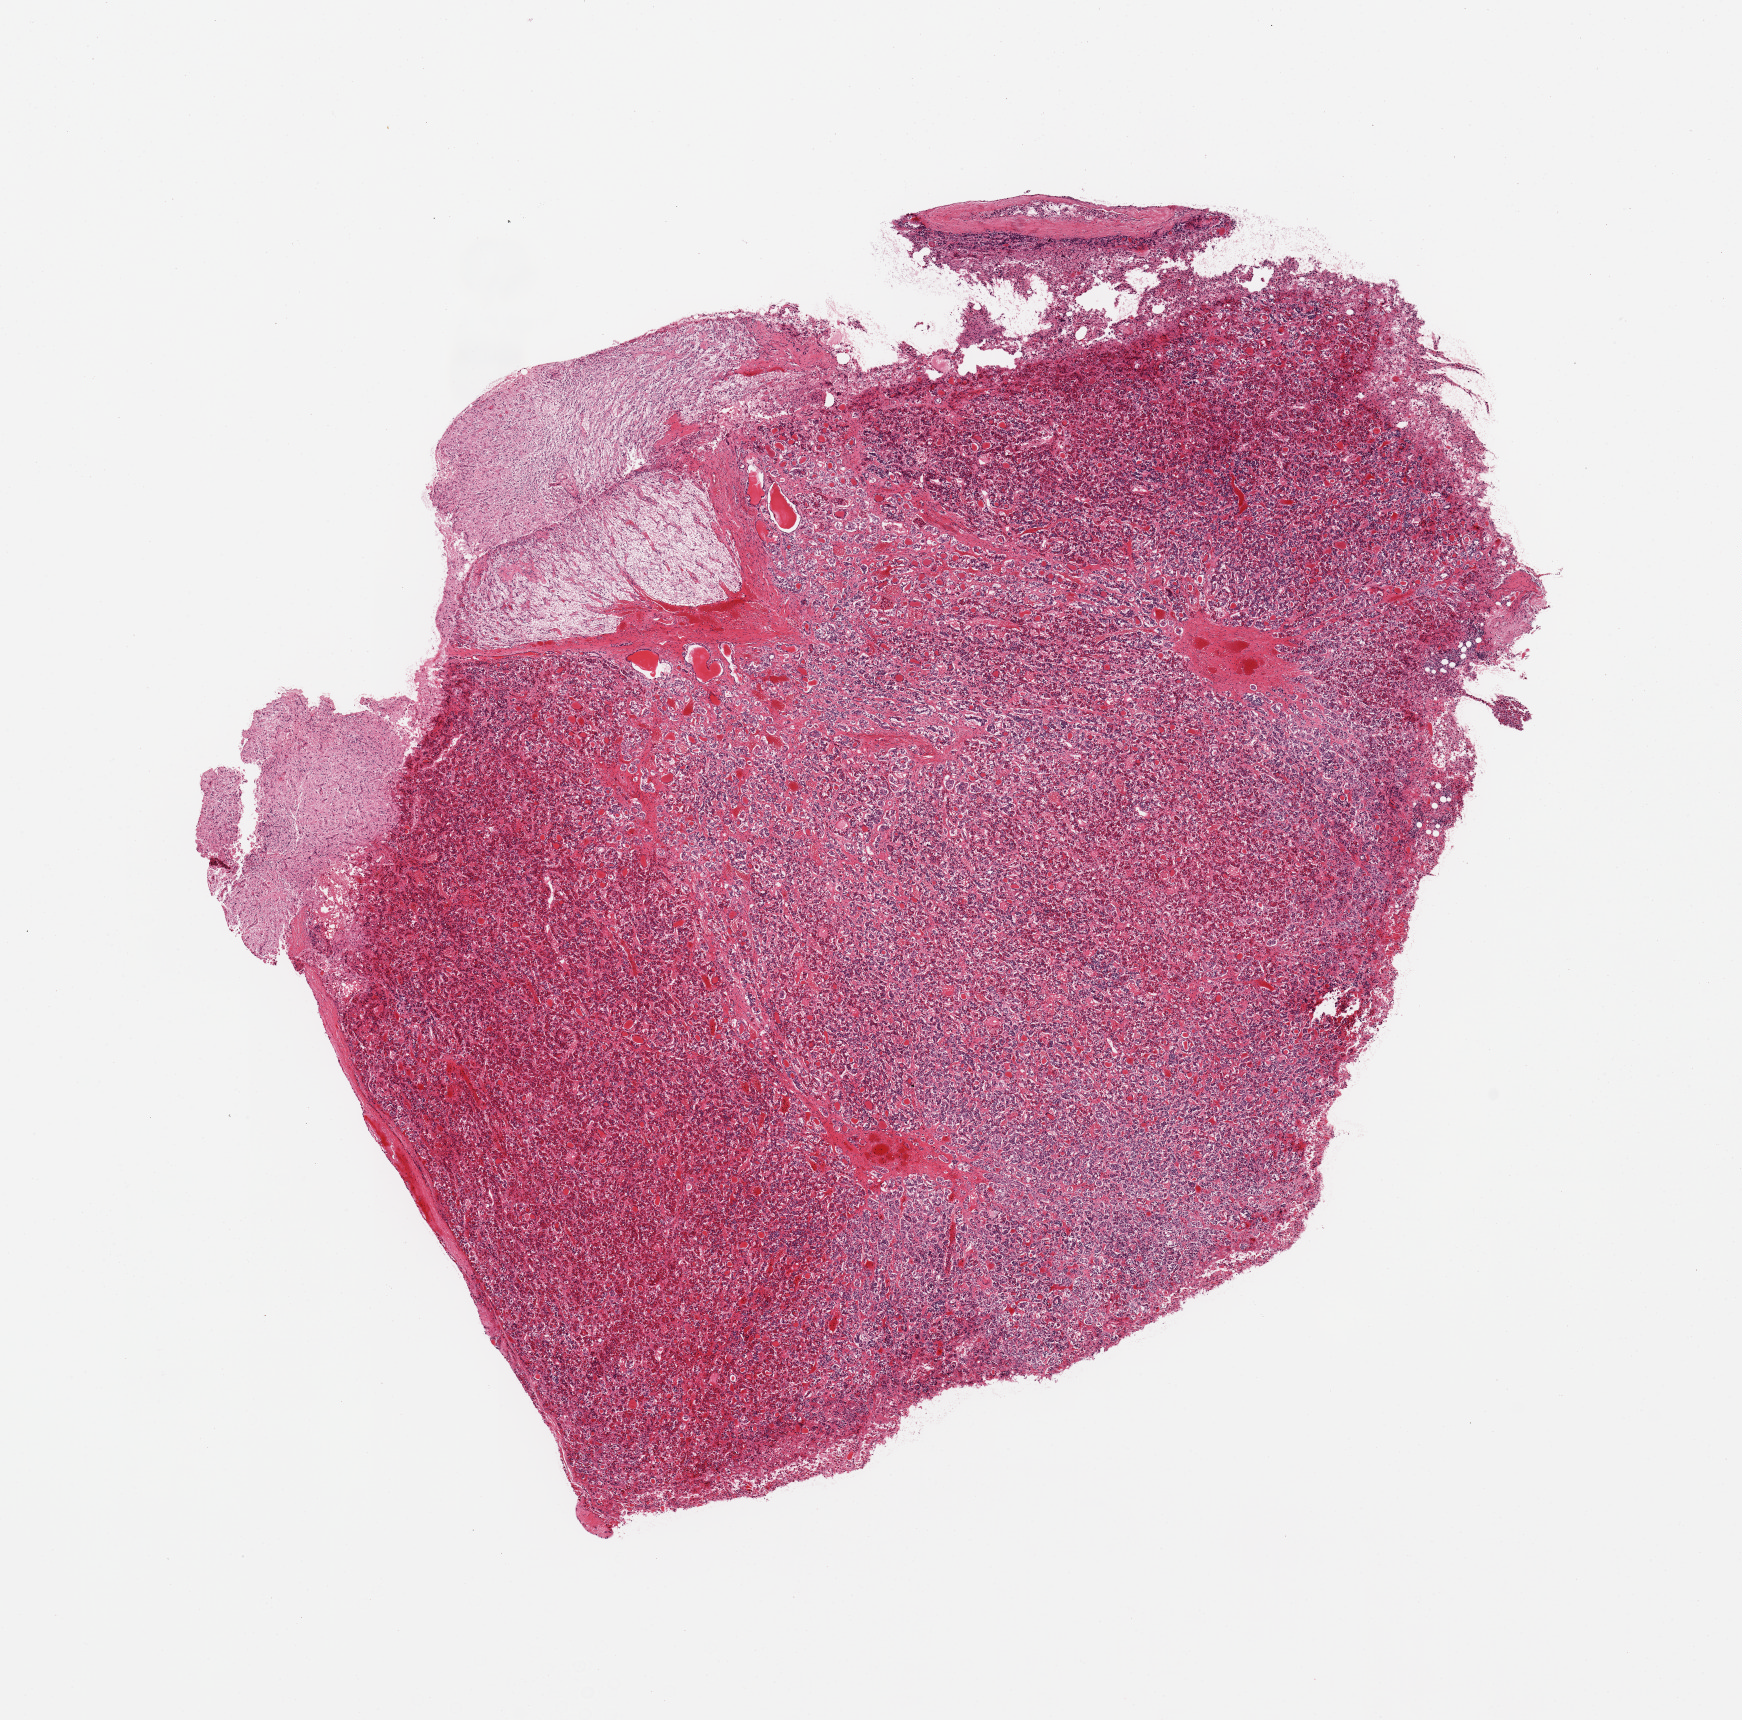
Hematoxylin and eosin (H&E) whole-slide image, brightfield — whole scanned area (about 13.8 x 13.6 mm) shown as a low-resolution overview; PAXgene-fixed, paraffin-embedded tissue; section of pituitary (target tissue); donor tissue sample. Donor: female.
Pathologist's review note for this sample: 1 pieces; adenohypophysis and neurohypophysis.